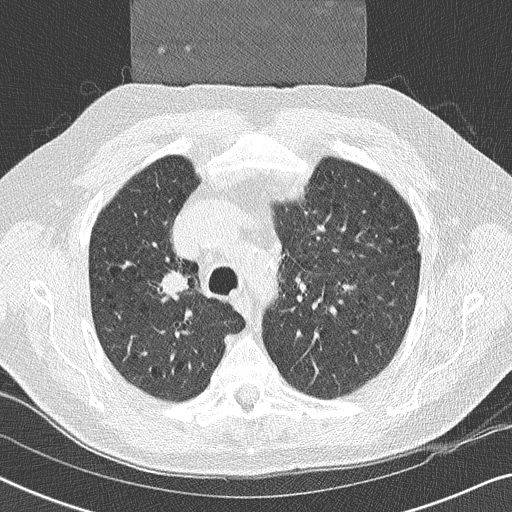
Axial slice from a low-dose chest CT screening exam. Second screening round (one year after baseline). Lung window (W 1500 / L -600 HU). 2 mm slice thickness. Lung (sharp) reconstruction kernel (B50f). Male, age 59 years at enrolment.
• Expert-annotated lung lesion, box from (x=146, y=257) to (x=205, y=308) px.
• Screening reader's record for this exam (one nodule recorded; not confirmed to be the boxed lesion): non-calcified nodule or mass ≥4 mm, right upper lobe, 17 × 16 mm, smooth margins, soft tissue attenuation, pre-existing on the prior screen: yes.
• Participant outcome: lung cancer diagnosed 14 days after this screen — squamous cell carcinoma, NOS, right upper lobe, poorly differentiated (G3), stage IIA (AJCC 6th edition), 20 mm at pathology.